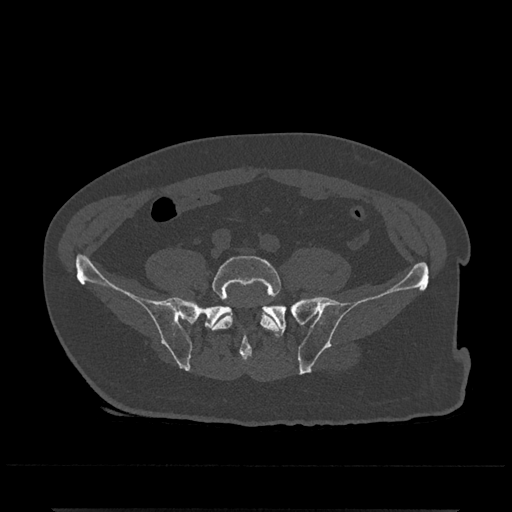
CT including the spine, one axial slice; position 61 of 797 along the scan axis; reconstruction kernel Br40s/3; bone window (W 1800 / L 400 HU); 0.5 mm slice thickness; 512 × 512 image matrix, field of view 393 × 393 mm. Patient: male, 67 years. From the clinical record (not read from this slice): primary cancer: prostate.
Annotated regions visible in this slice (semi-automatic segmentation, software-assisted and operator-edited):
- L5 vertebra: bounding box (x1, y1, x2, y2) in pixels: (210, 255, 281, 332)